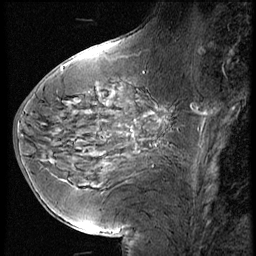
Breast MRI (dynamic contrast-enhanced), one sagittal slice; position 24 of 60 along the scan axis; 3 images stored at this slice position (order not interpretable as contrast timing); 1.5 T; TE 4.2 ms, TR 9 ms; 256 × 256 image matrix. Female patient, age 56 years. Case-level facts recorded for this patient, not image findings: setting: breast cancer imaged before/during neoadjuvant chemotherapy.
Structures marked on this image (semi-automatic segmentation, software-assisted and operator-edited):
- analysis volume of interest (the breast-tissue region the enhancement analysis was run in; not a lesion): box from (x=137, y=61) to (x=218, y=137) px
- tumour enhancement mask (voxels above the 140 % enhancement threshold inside the analysis volume of interest): (x=192, y=104)–(x=208, y=114)